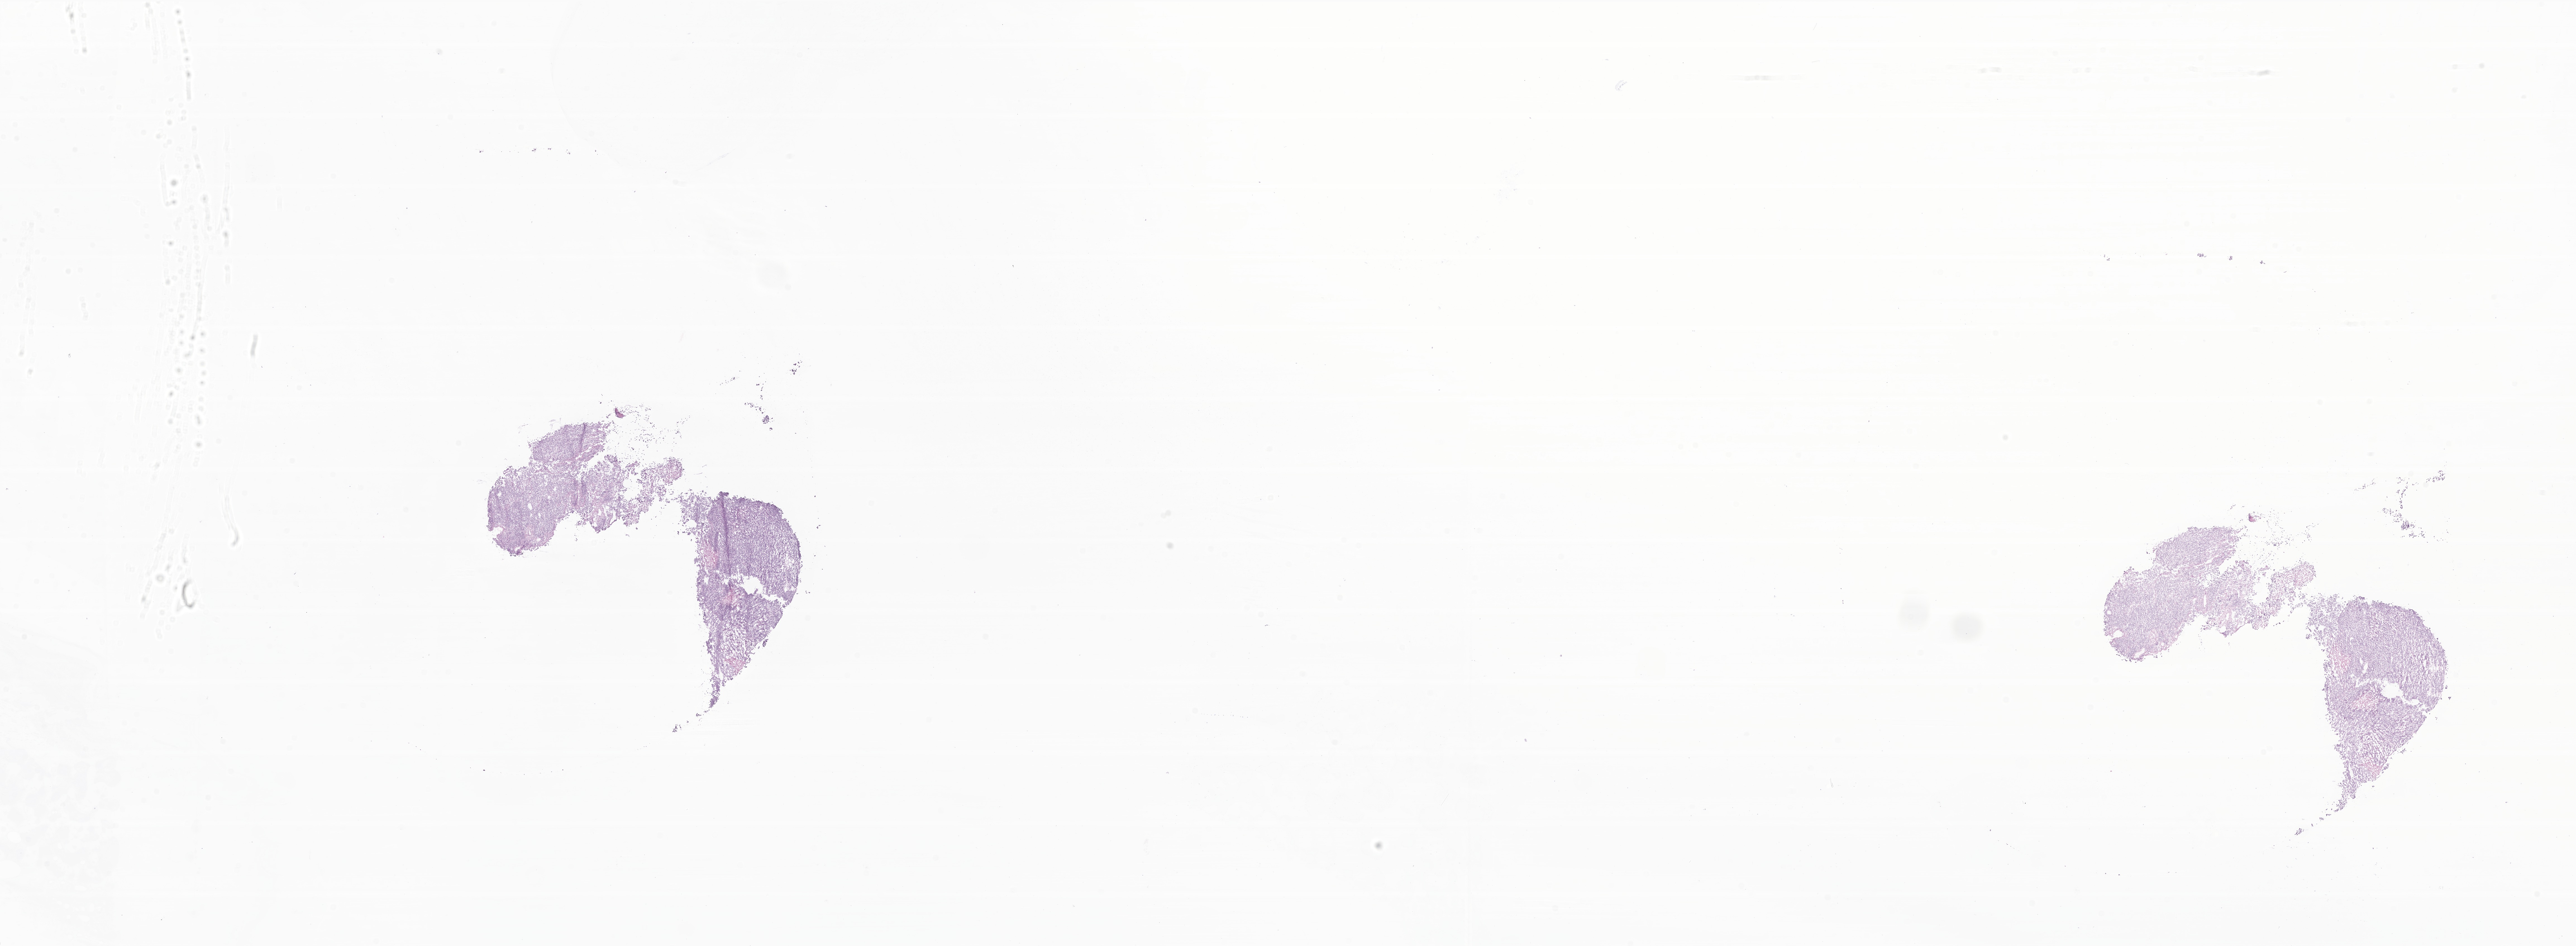
H&E whole-slide image of tumor tissue from the ovary — low-resolution overview of the scanned area, about 38.9 x 14.3 mm. Cryosection (OCT / tissue freezing medium). Patient female; age 178 months (14 years 10 months).
- recorded diagnosis: Sarcoma, NOS